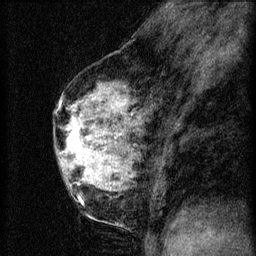
Breast MRI (dynamic contrast-enhanced), one sagittal slice. Slice 36 of 60 in the series (ordered by position). 3 images stored at this slice position (order not interpretable as contrast timing). 1.5 T. TE 4.2 ms, TR 8.2 ms. 2 mm slice thickness. 256 × 256 image matrix. Female patient, age 56 years.
Structures marked on this image (semi-automatic segmentation, software-assisted and operator-edited):
- analysis volume of interest (the breast-tissue region the enhancement analysis was run in; not a lesion): bounding box (x1, y1, x2, y2) in pixels: (60, 124, 114, 179)
- tumour enhancement mask (voxels above the 70 % enhancement threshold inside the analysis volume of interest): (67, 124, 102, 169)